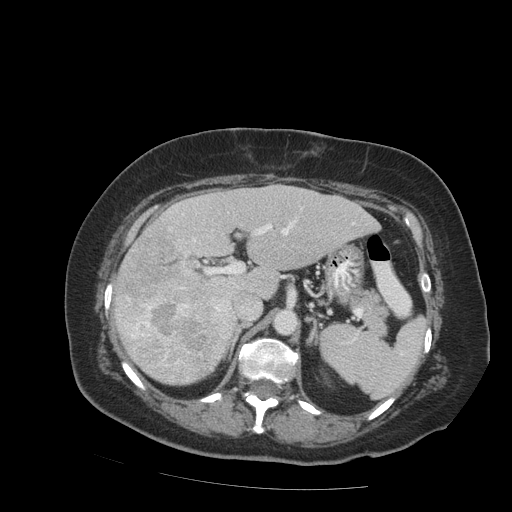
Contrast-enhanced abdominal CT (liver protocol), one axial slice; position 51 of 99 along the scan axis; reconstruction kernel STANDARD; soft-tissue window (W 400 / L 40 HU); 2.5 mm slice thickness; 512 × 512 image matrix, field of view 400 × 400 mm. From the clinical record (not read from this slice): diagnosis: hepatocellular carcinoma (patient treated with transarterial chemoembolisation; whether this scan precedes or follows treatment is not stated here); TNM stage (as recorded): Stage-IVB; Child-Pugh class: A.
Structures marked on this image (semi-automatic segmentation, software-assisted and operator-edited):
- liver parenchyma outside the tumour (the mass and vessels are separate outlines, so this box may not span the whole liver): bounding box <112,184,380,384> (left, top, right, bottom; pixels)
- mass: <112,226,230,384>
- liver vessels: <182,213,355,313>